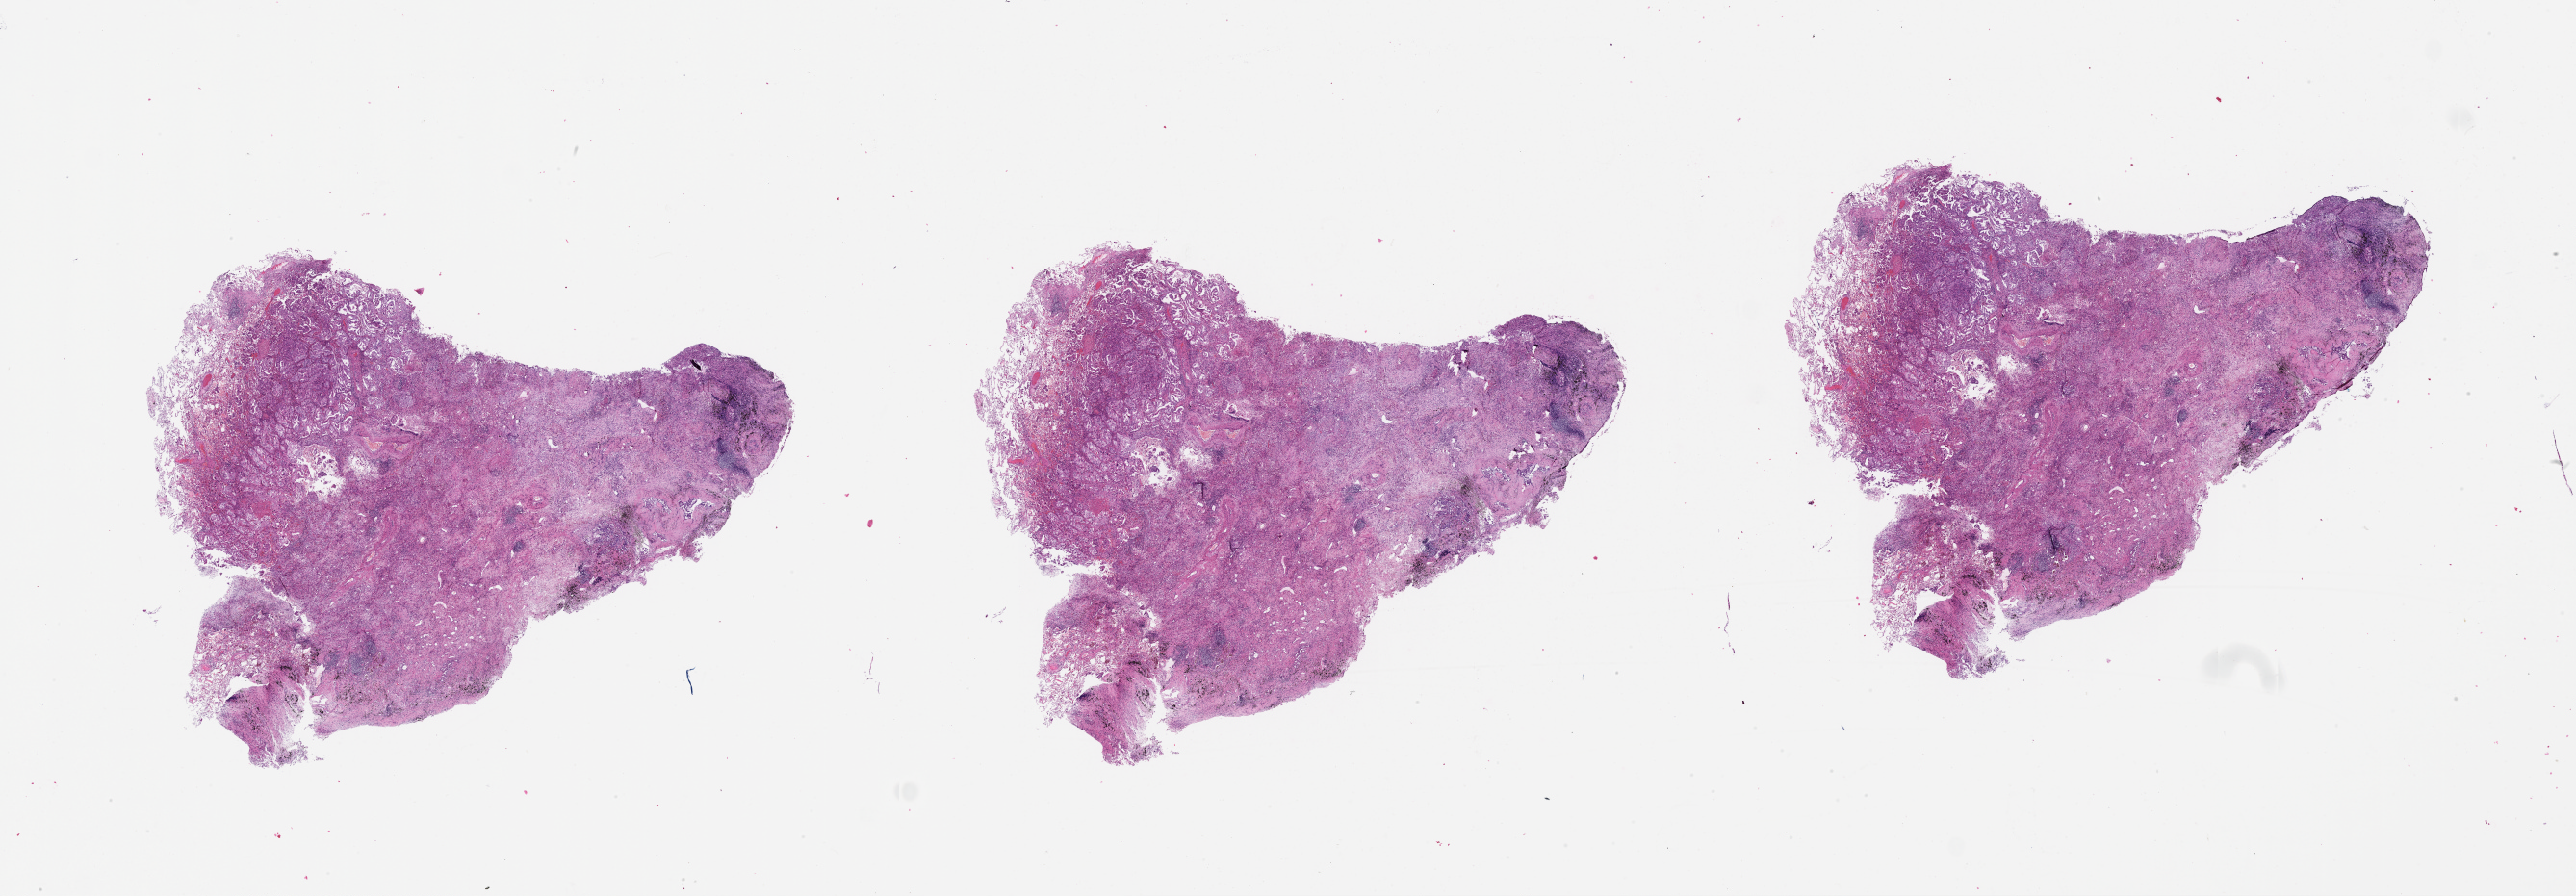
Digitized H&E-stained tissue section (whole slide), shown as a low-resolution overview of the whole scanned area (about 43.1 x 15.0 mm), lung, tissue type not recorded.
- patient diagnosis (cohort enrolment): lung adenocarcinoma (lung)